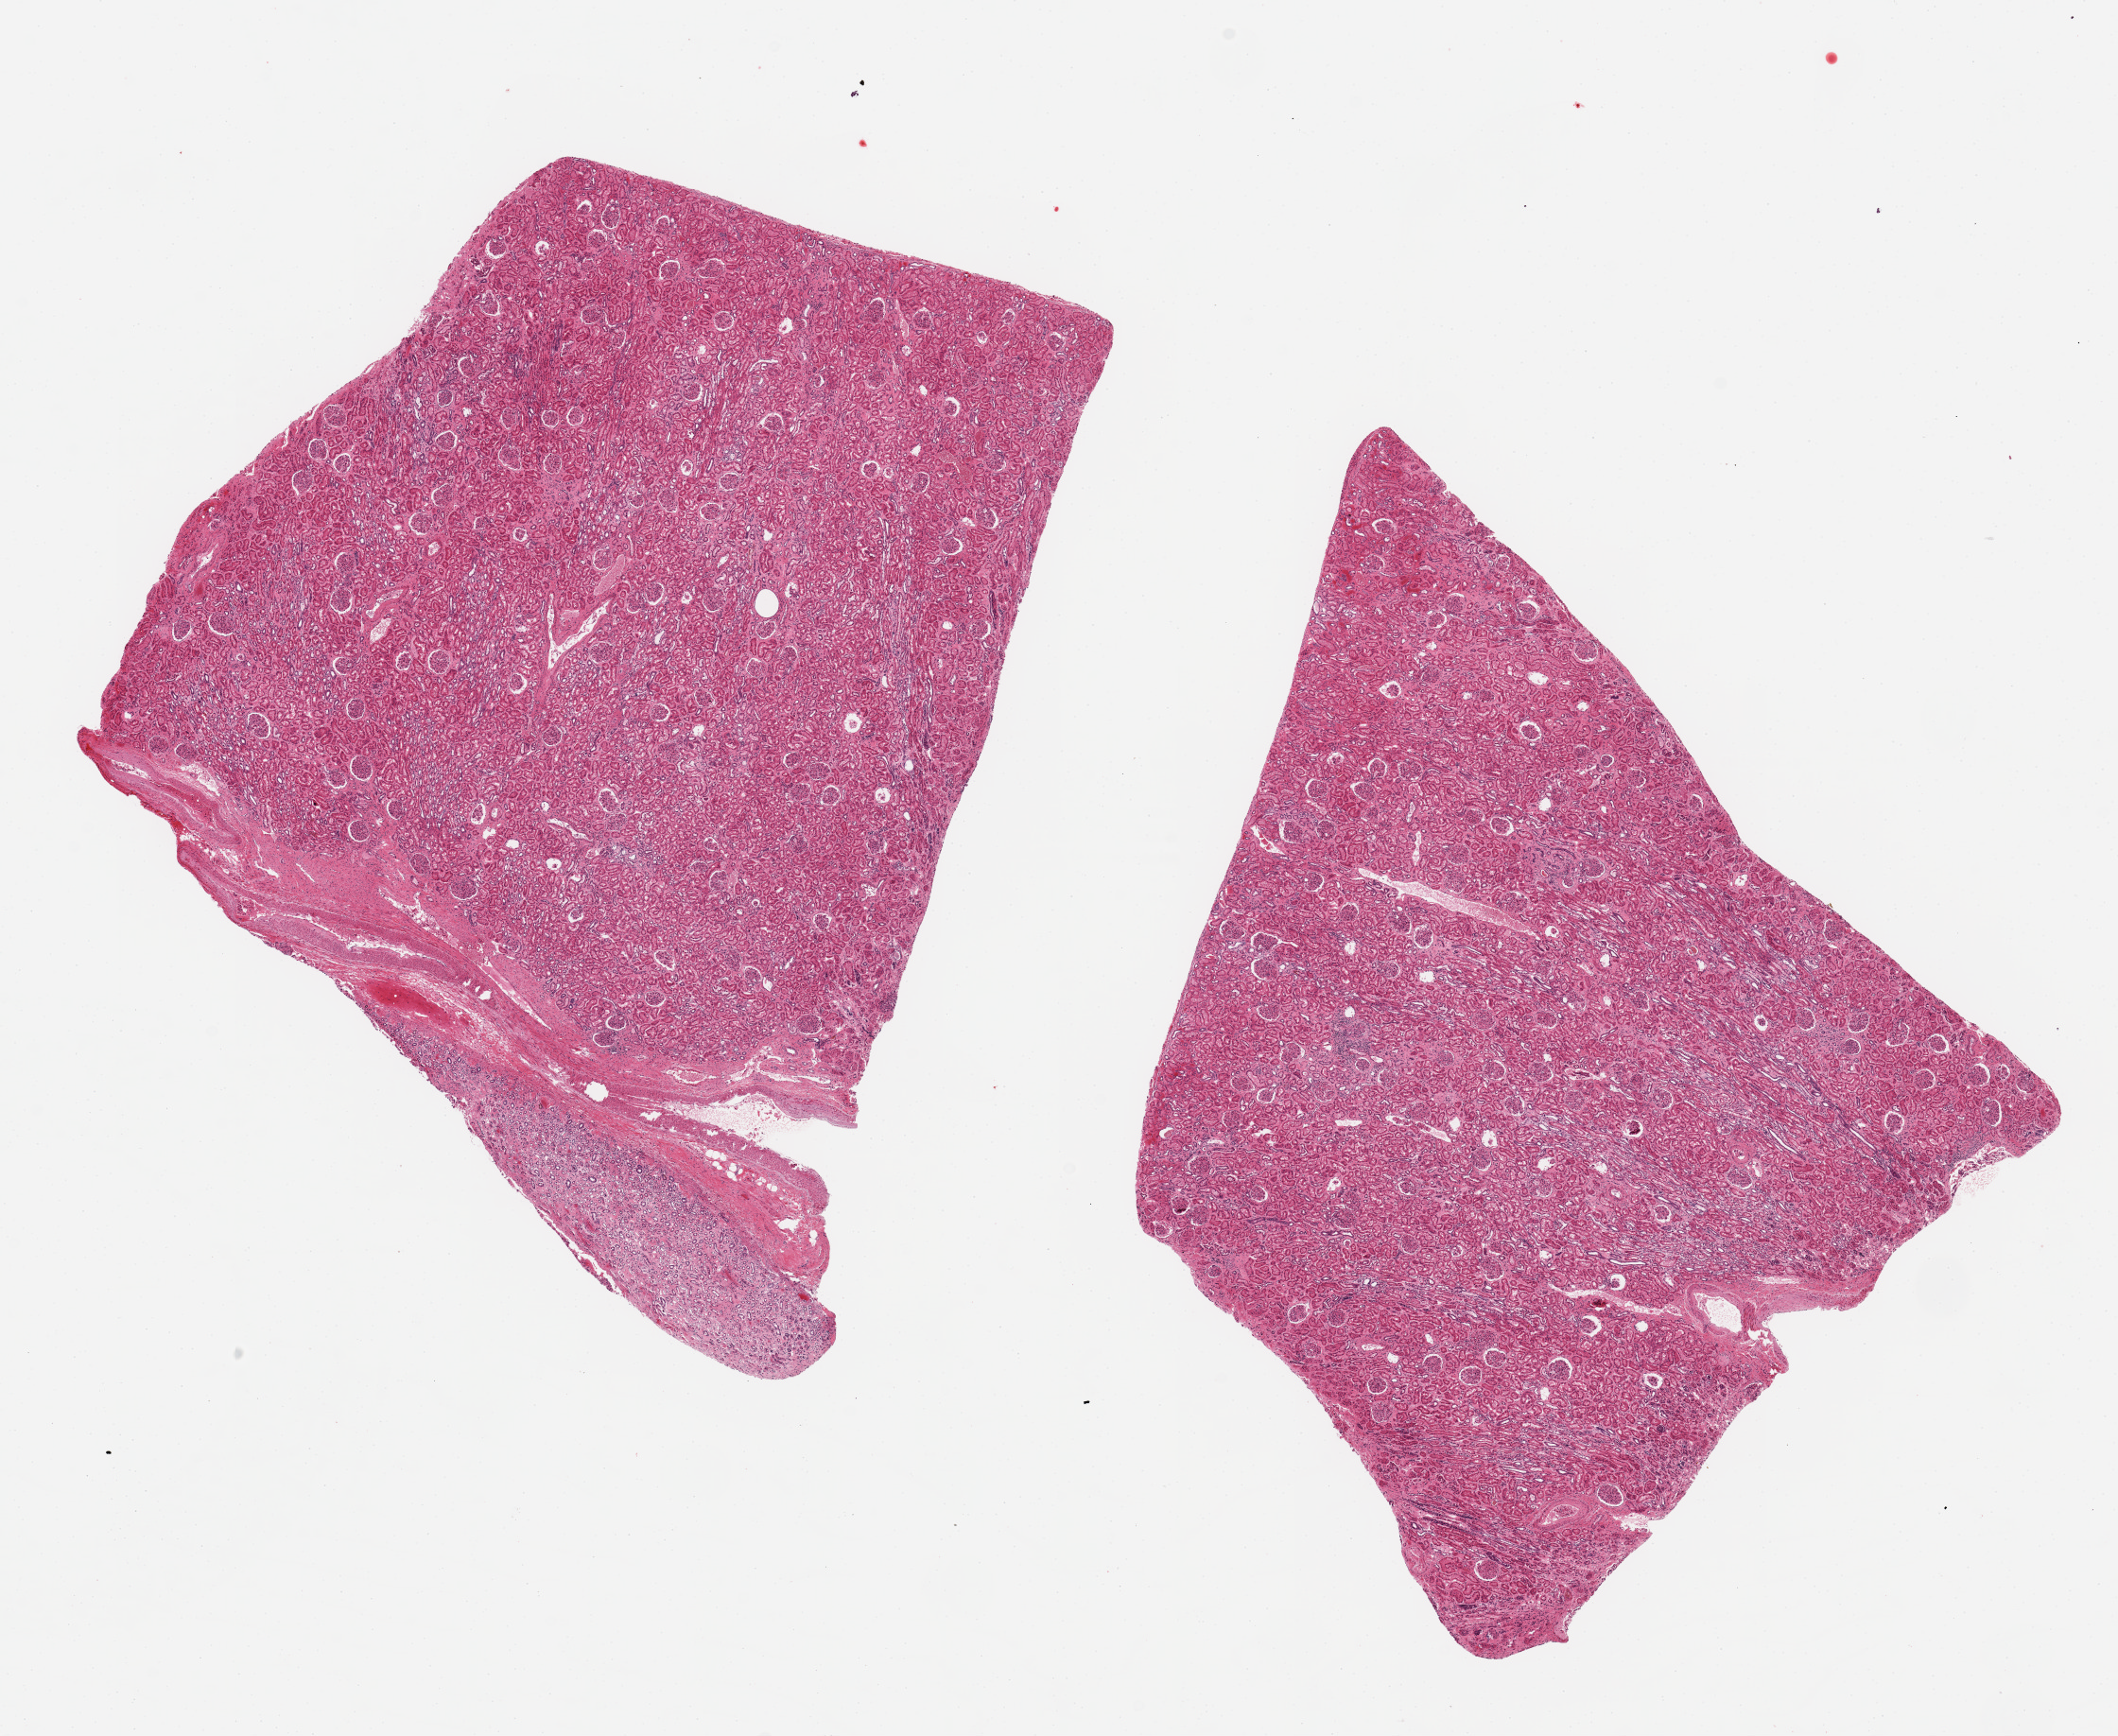
Whole-slide image, H&E stain, whole scanned area (about 17.7 x 14.5 mm, slide scanned at 20x) shown as a low-resolution overview; PAXgene-fixed paraffin-embedded (PFPE) section; target tissue: renal cortex; donor tissue sample.
Review note (as recorded): 2 ~7x7mm aliquots; one all cortex, one is 90% cortex and 10% medulla???may be used if reclassified as renal cortex. Glomeruli and tubules reasonably well preserved.